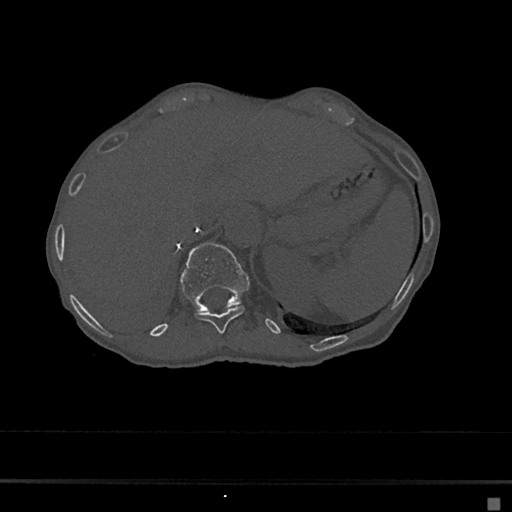
CT including the spine, one axial slice. Position 151 of 797 along the scan axis. Reconstruction kernel Br40s/3. 120 kVp. Bone window (W 1800 / L 400 HU). 0.5 mm slice thickness. 512 × 512 image matrix, field of view 360 × 360 mm. Female patient, age 68 years. From the clinical record (not read from this slice): primary cancer: renal.
Structures marked on this image (semi-automatically segmented with operator editing):
- T11 vertebra: bounding box (x1, y1, x2, y2) in pixels: (195, 304, 245, 334)
- T12 vertebra: (180, 243, 249, 312)